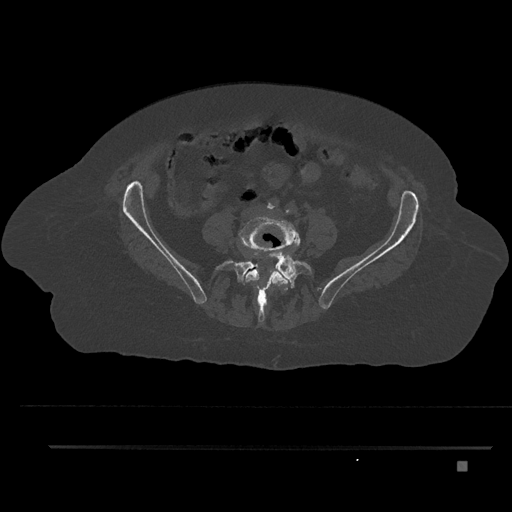
CT including the spine, one axial slice; position 55 of 797 along the scan axis; 120 kVp; bone window (W 1800 / L 400 HU); 0.5 mm slice thickness; 512 × 512 image matrix, field of view 437 × 437 mm. Female patient, age 76 years. From the clinical record (not read from this slice): primary cancer: lung; vertebrae with lytic lesions (as recorded): T11, L3.
Annotated regions visible in this slice (semi-automatically segmented with operator editing):
- L4 vertebra: bounding box <240,215,300,312> (left, top, right, bottom; pixels)
- L5 vertebra: <215,245,312,323>